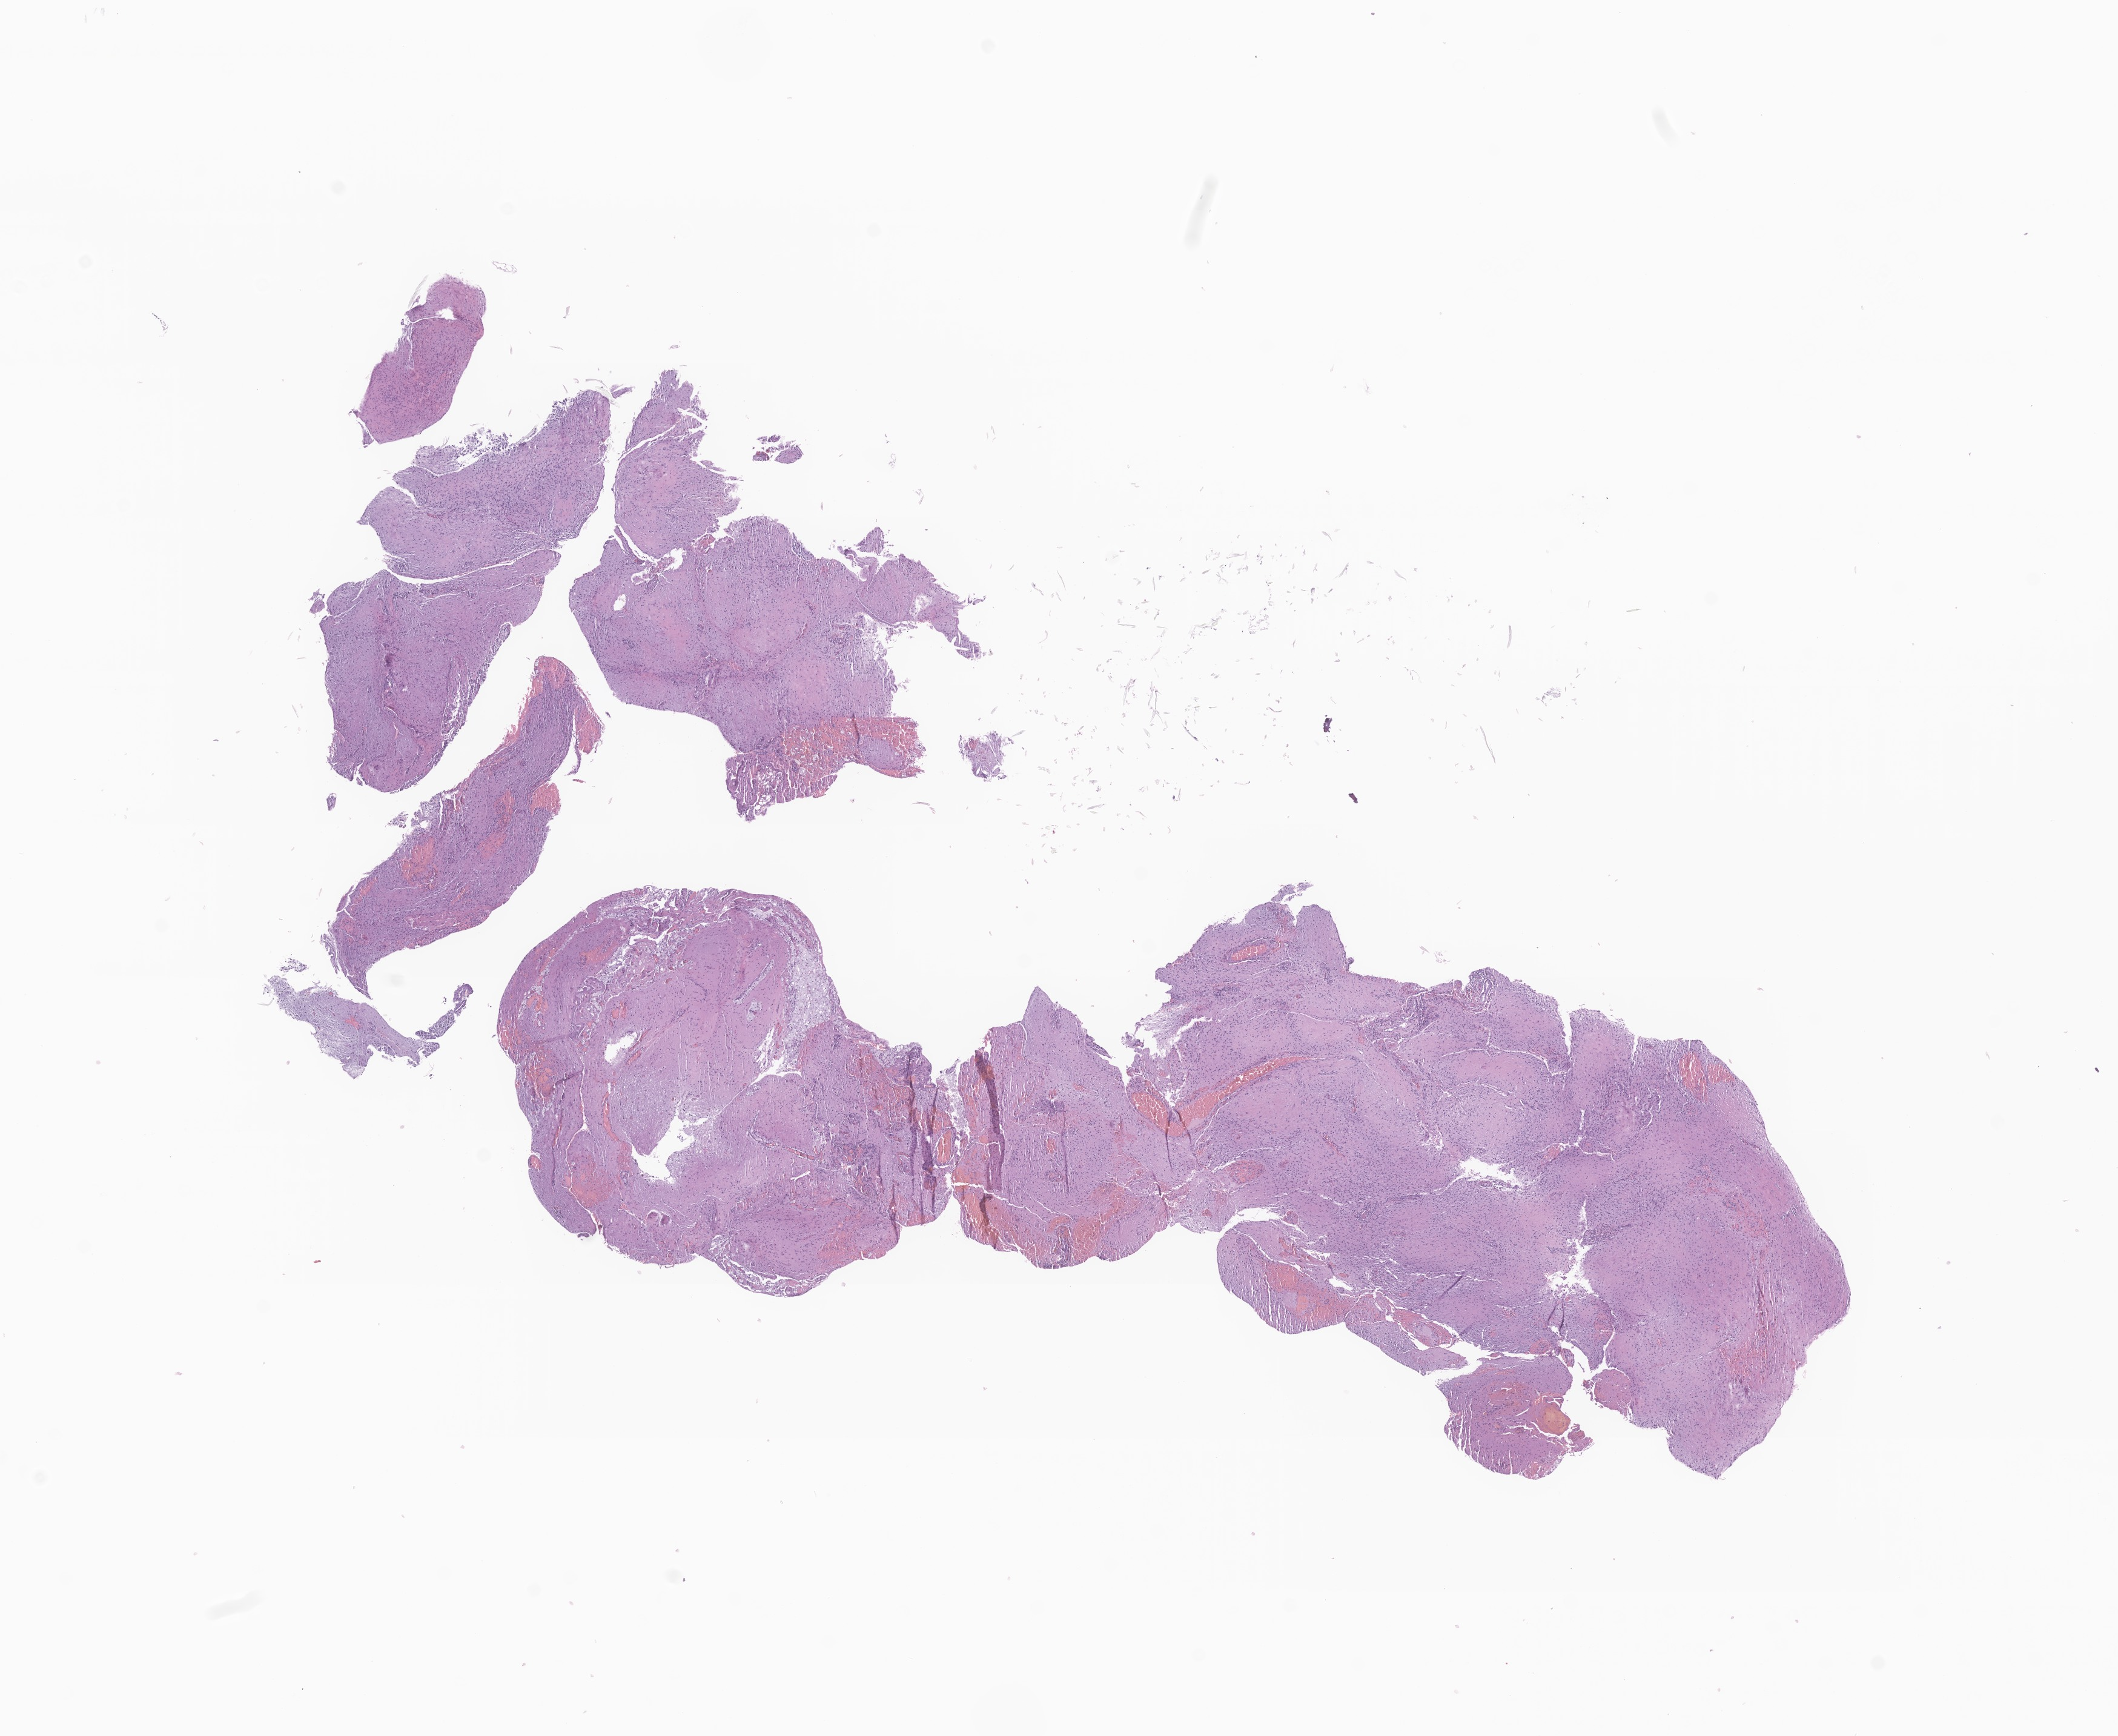
Whole-slide image, hematoxylin and eosin (H&E) stain of tumor tissue from the brain, a low-resolution overview of the entire scanned area, about 14.7 x 12.1 mm; formalin-fixed, paraffin-embedded (FFPE) tissue. Male patient, age 51 months (4 years 3 months).
- diagnosis: Glioma, malignant